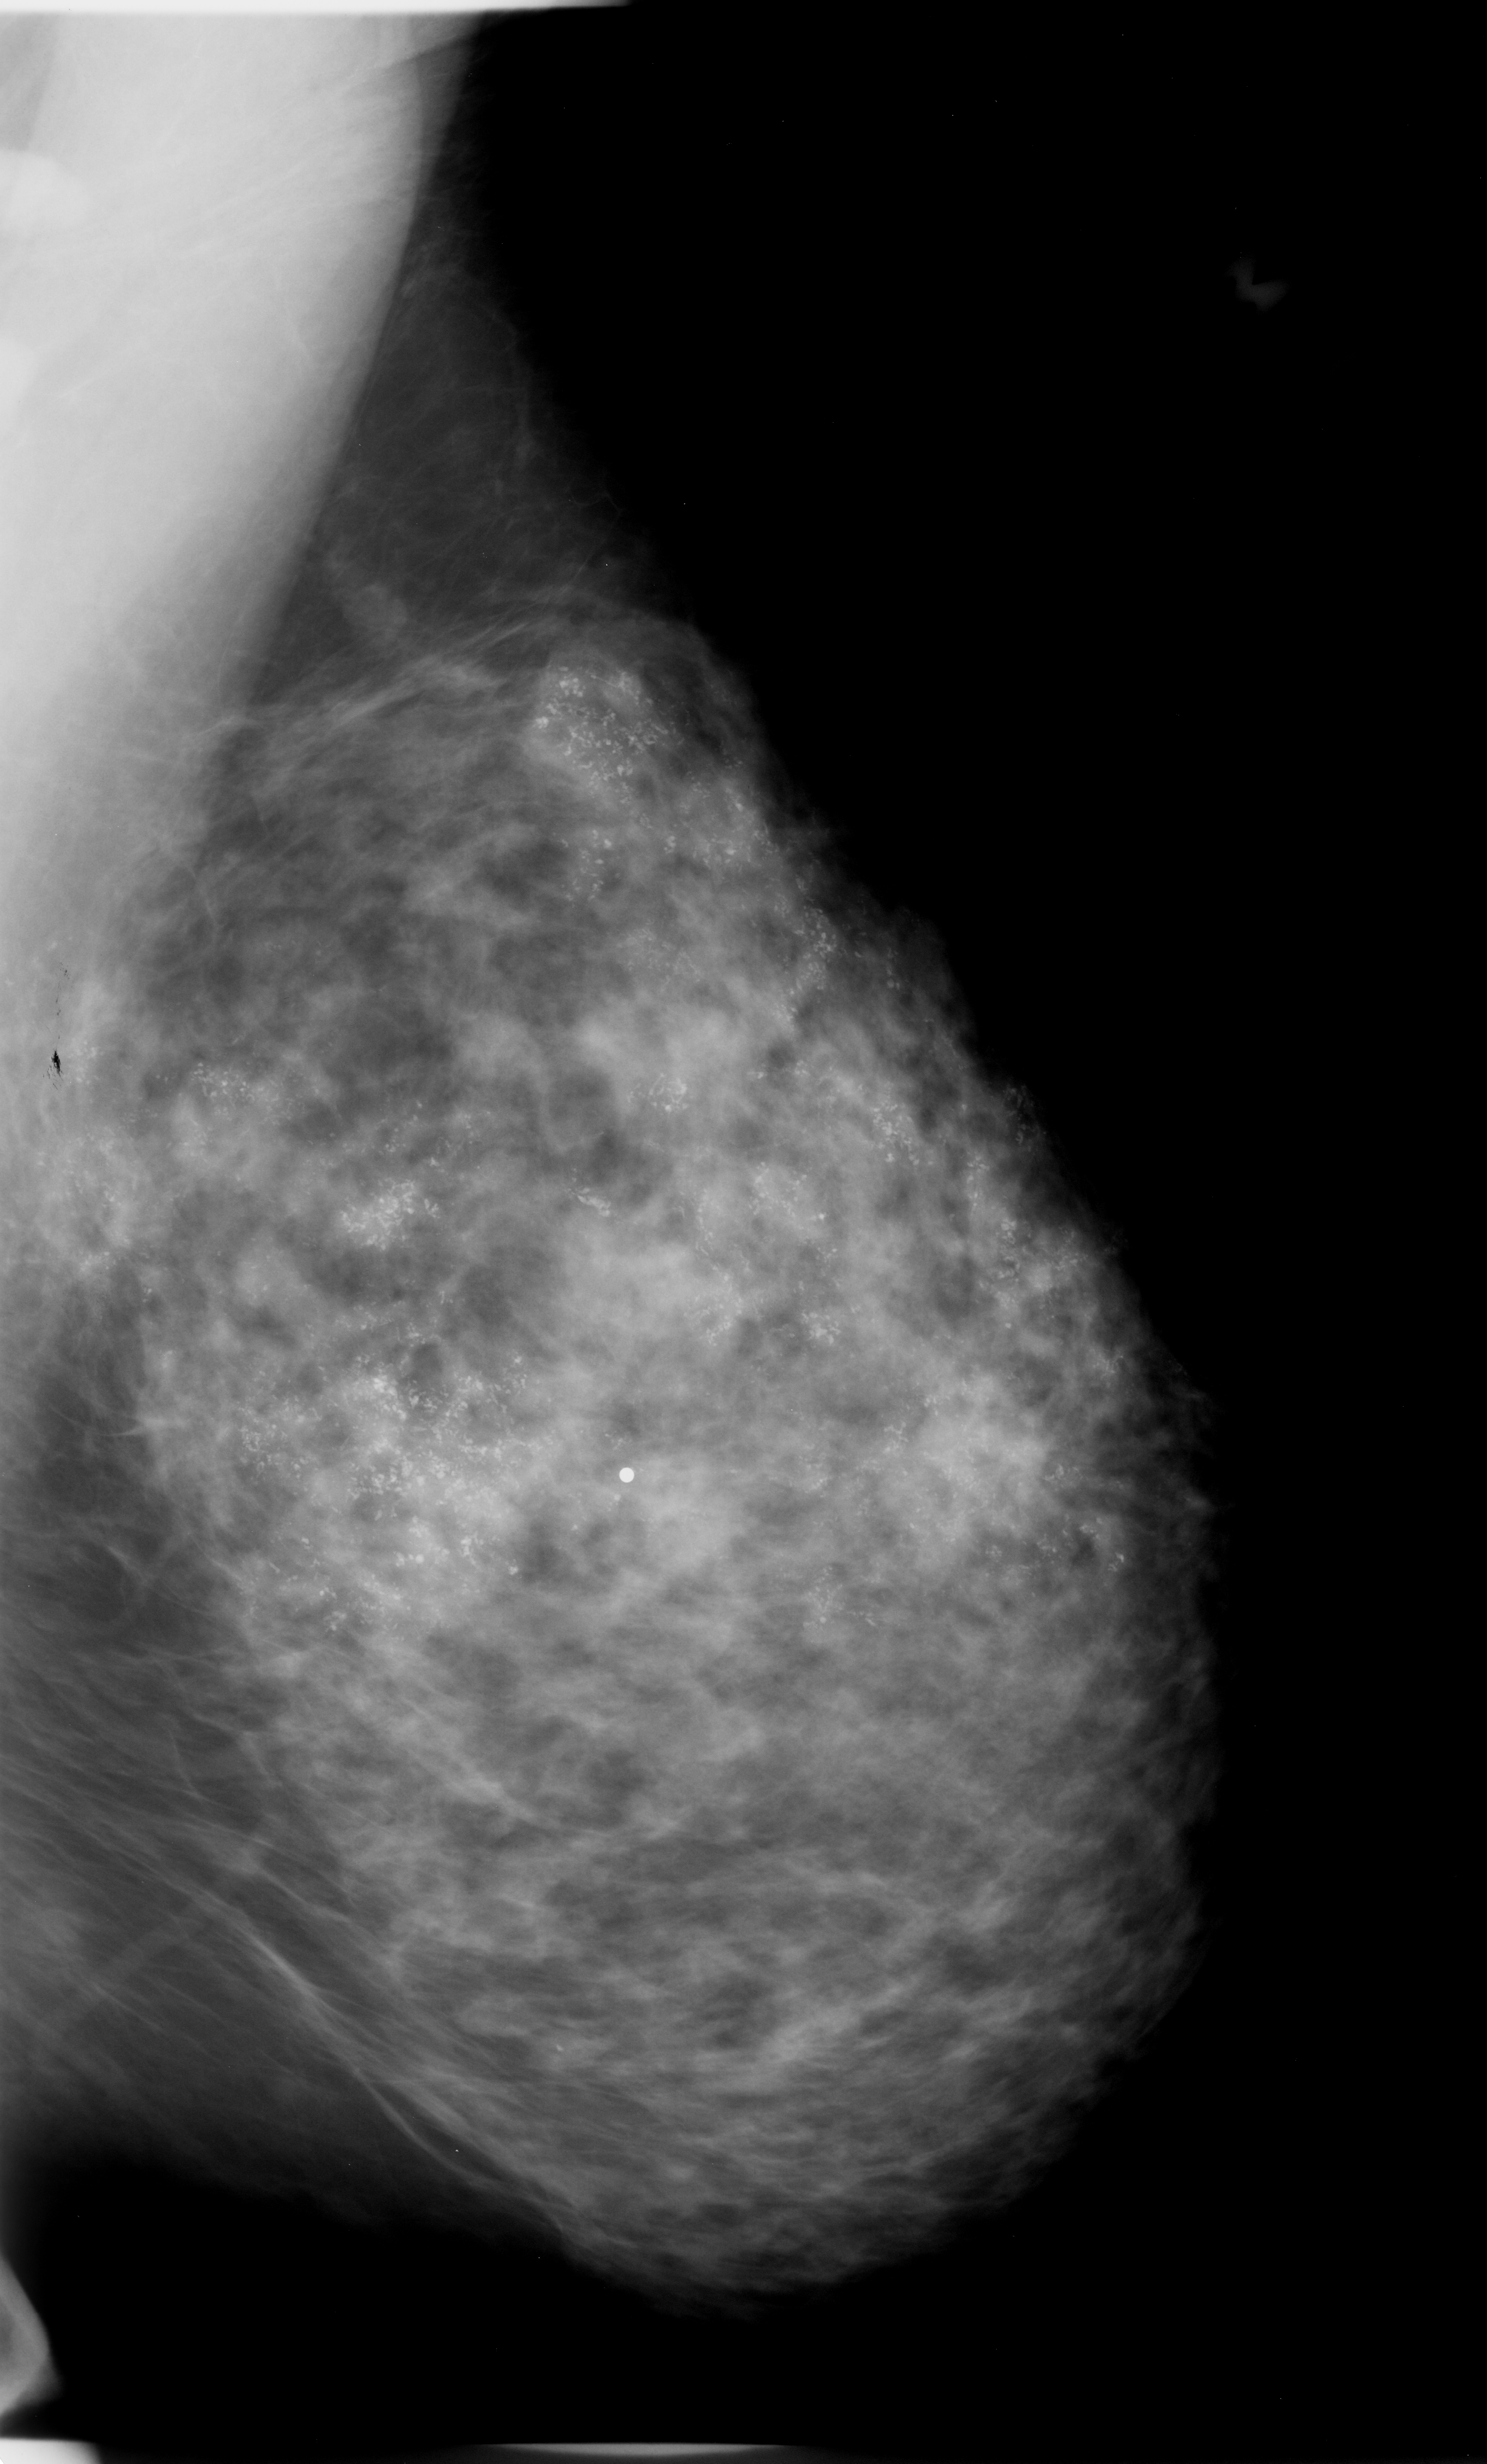
Digitized screen-film mammogram; left breast; mediolateral oblique (MLO) view; BI-RADS breast density category 3 (scale 1–4); 1487 × 2464 image matrix.
Expert-marked regions of interest on this film, with their recorded descriptors:
- calcifications, morphology pleomorphic, distribution regional; BI-RADS assessment category 5; subtlety rating 5 on a 1 (subtle) to 5 (obvious) scale; pathology (as recorded): malignant: box from (x=0, y=503) to (x=1197, y=1813) px